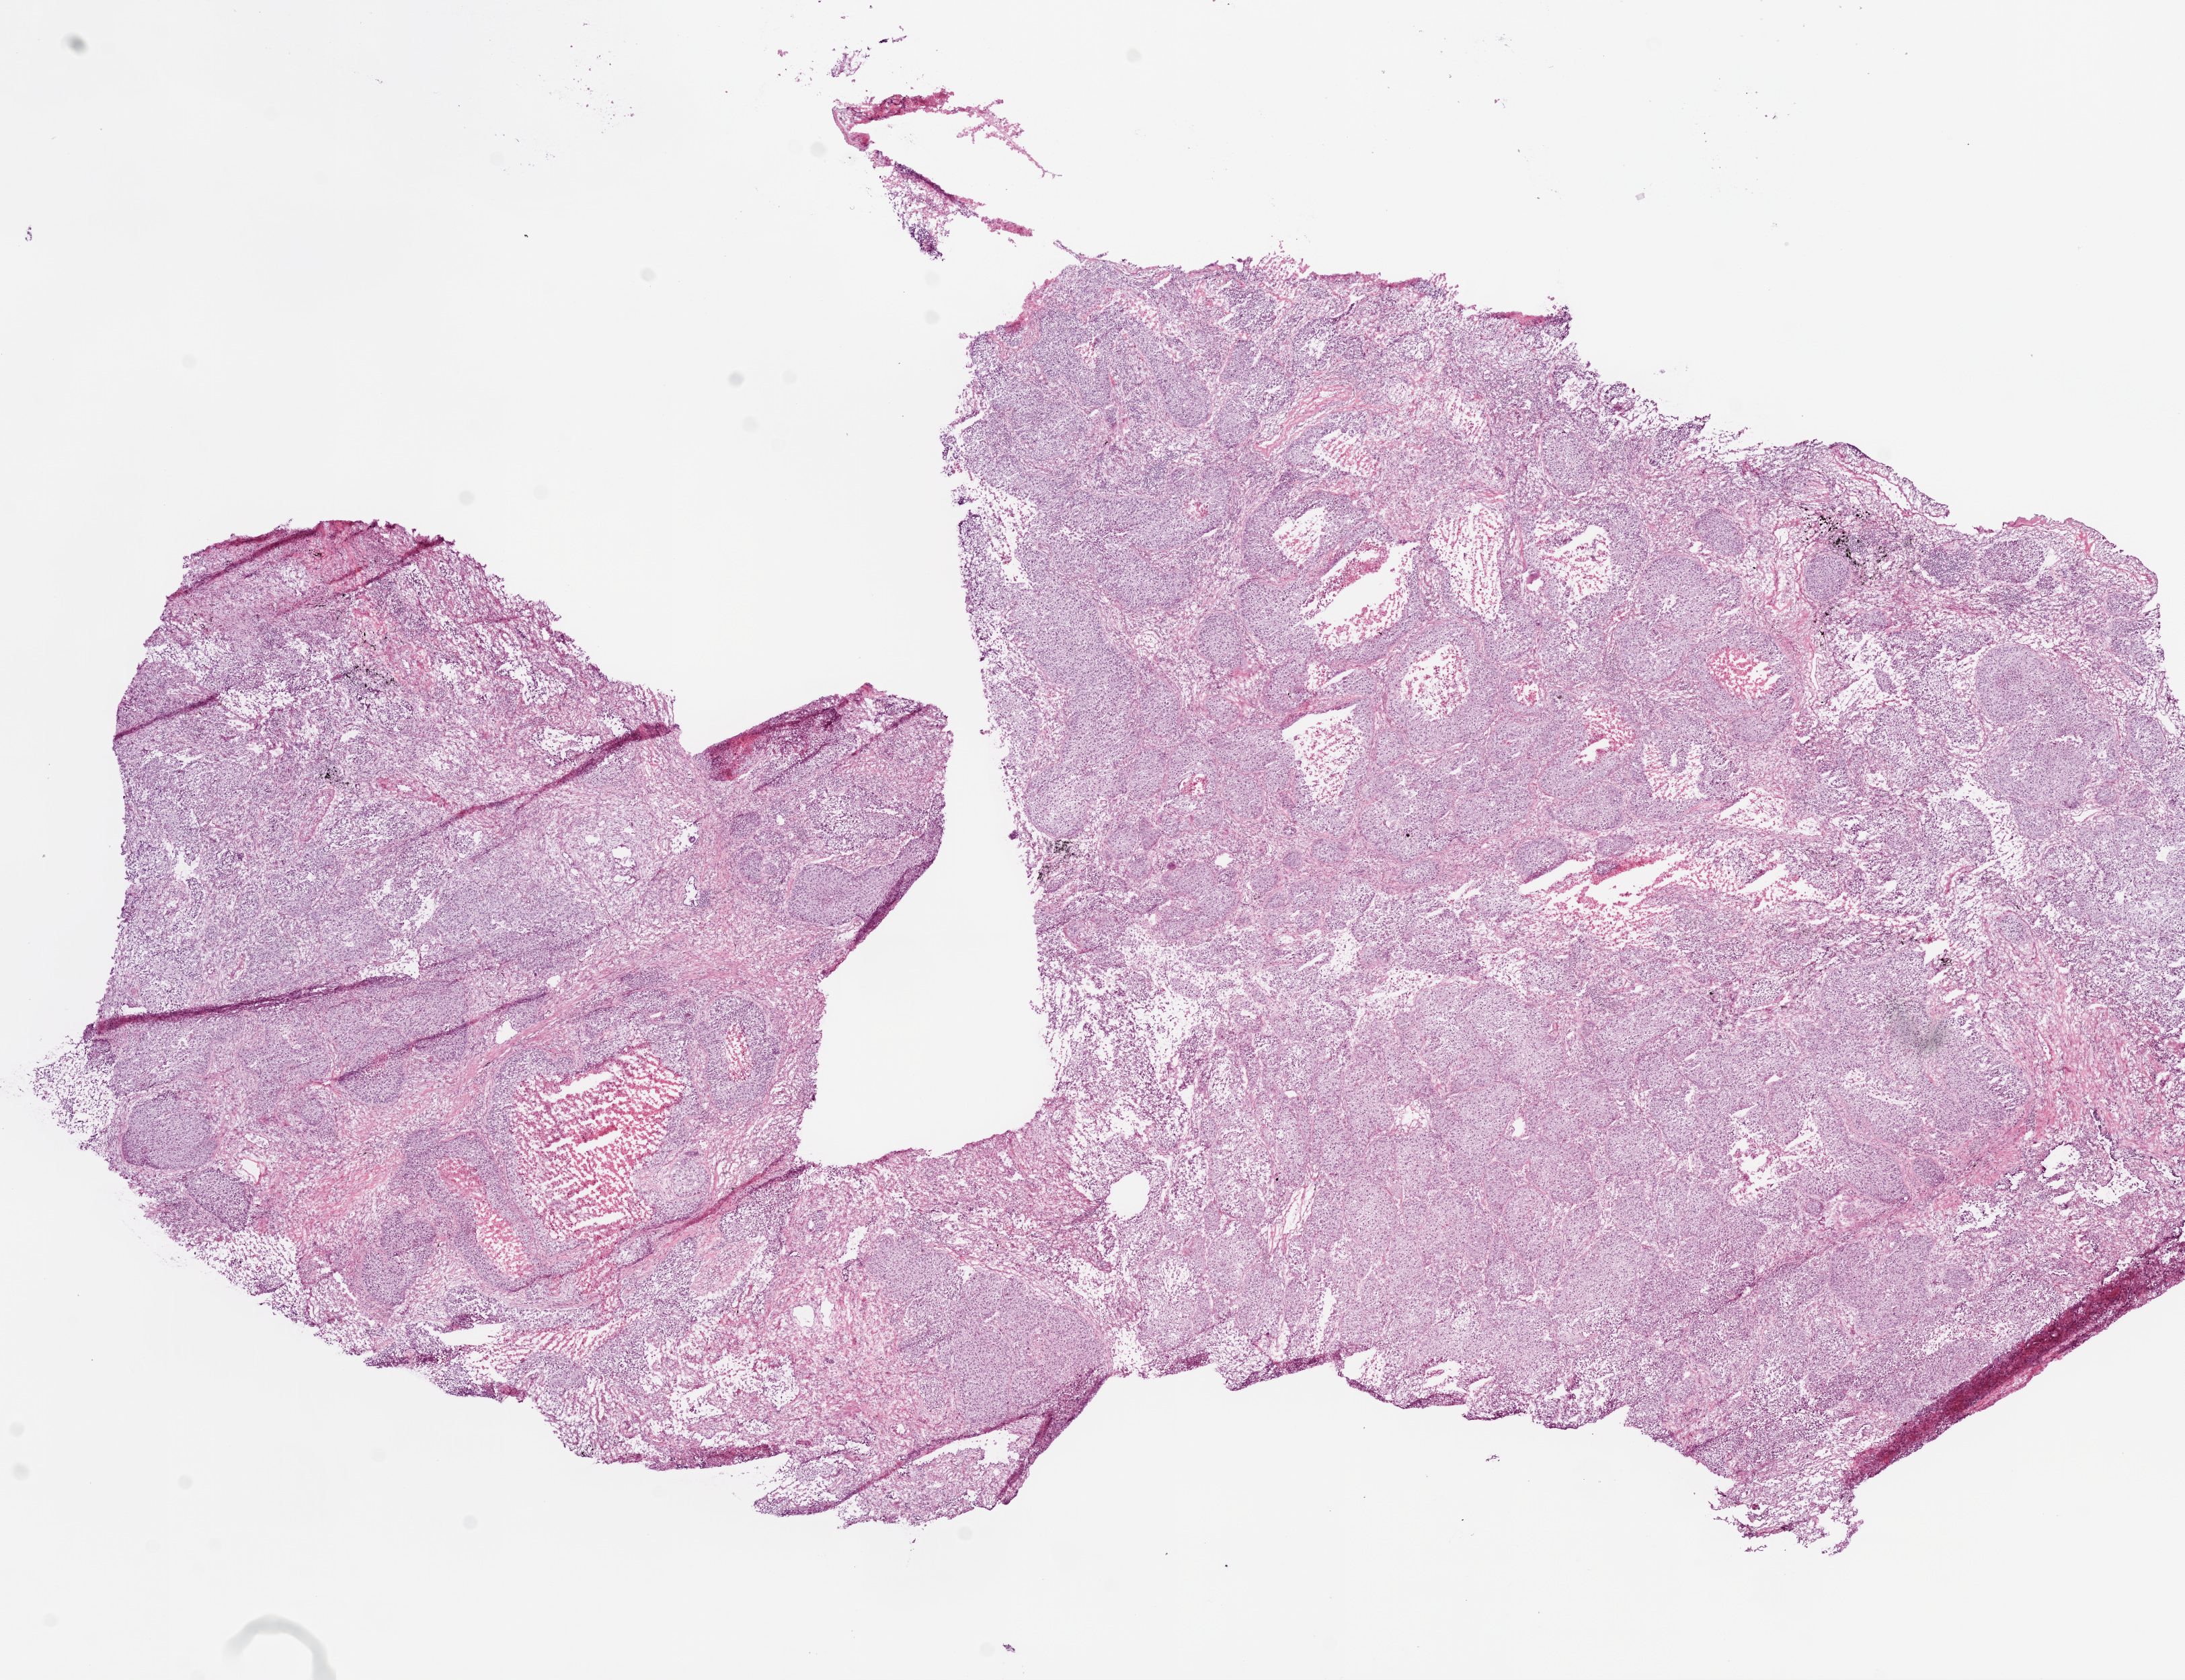
Digitized H&E-stained tissue section (whole slide) — a low-resolution overview of the entire scanned area, about 13.0 x 10.0 mm (acquisition: 20x scan), frozen section from the bottom of the tissue portion, primary tumour sample from the lung. Patient sex: male. Composition of this section per pathologist review: tumour cells 83%, tumour nuclei 80%, normal cells 2%, stromal cells 5%, necrosis 10%.
AJCC pathologic stage: IIB (6th edition). Diagnosis: Squamous cell carcinoma, NOS.